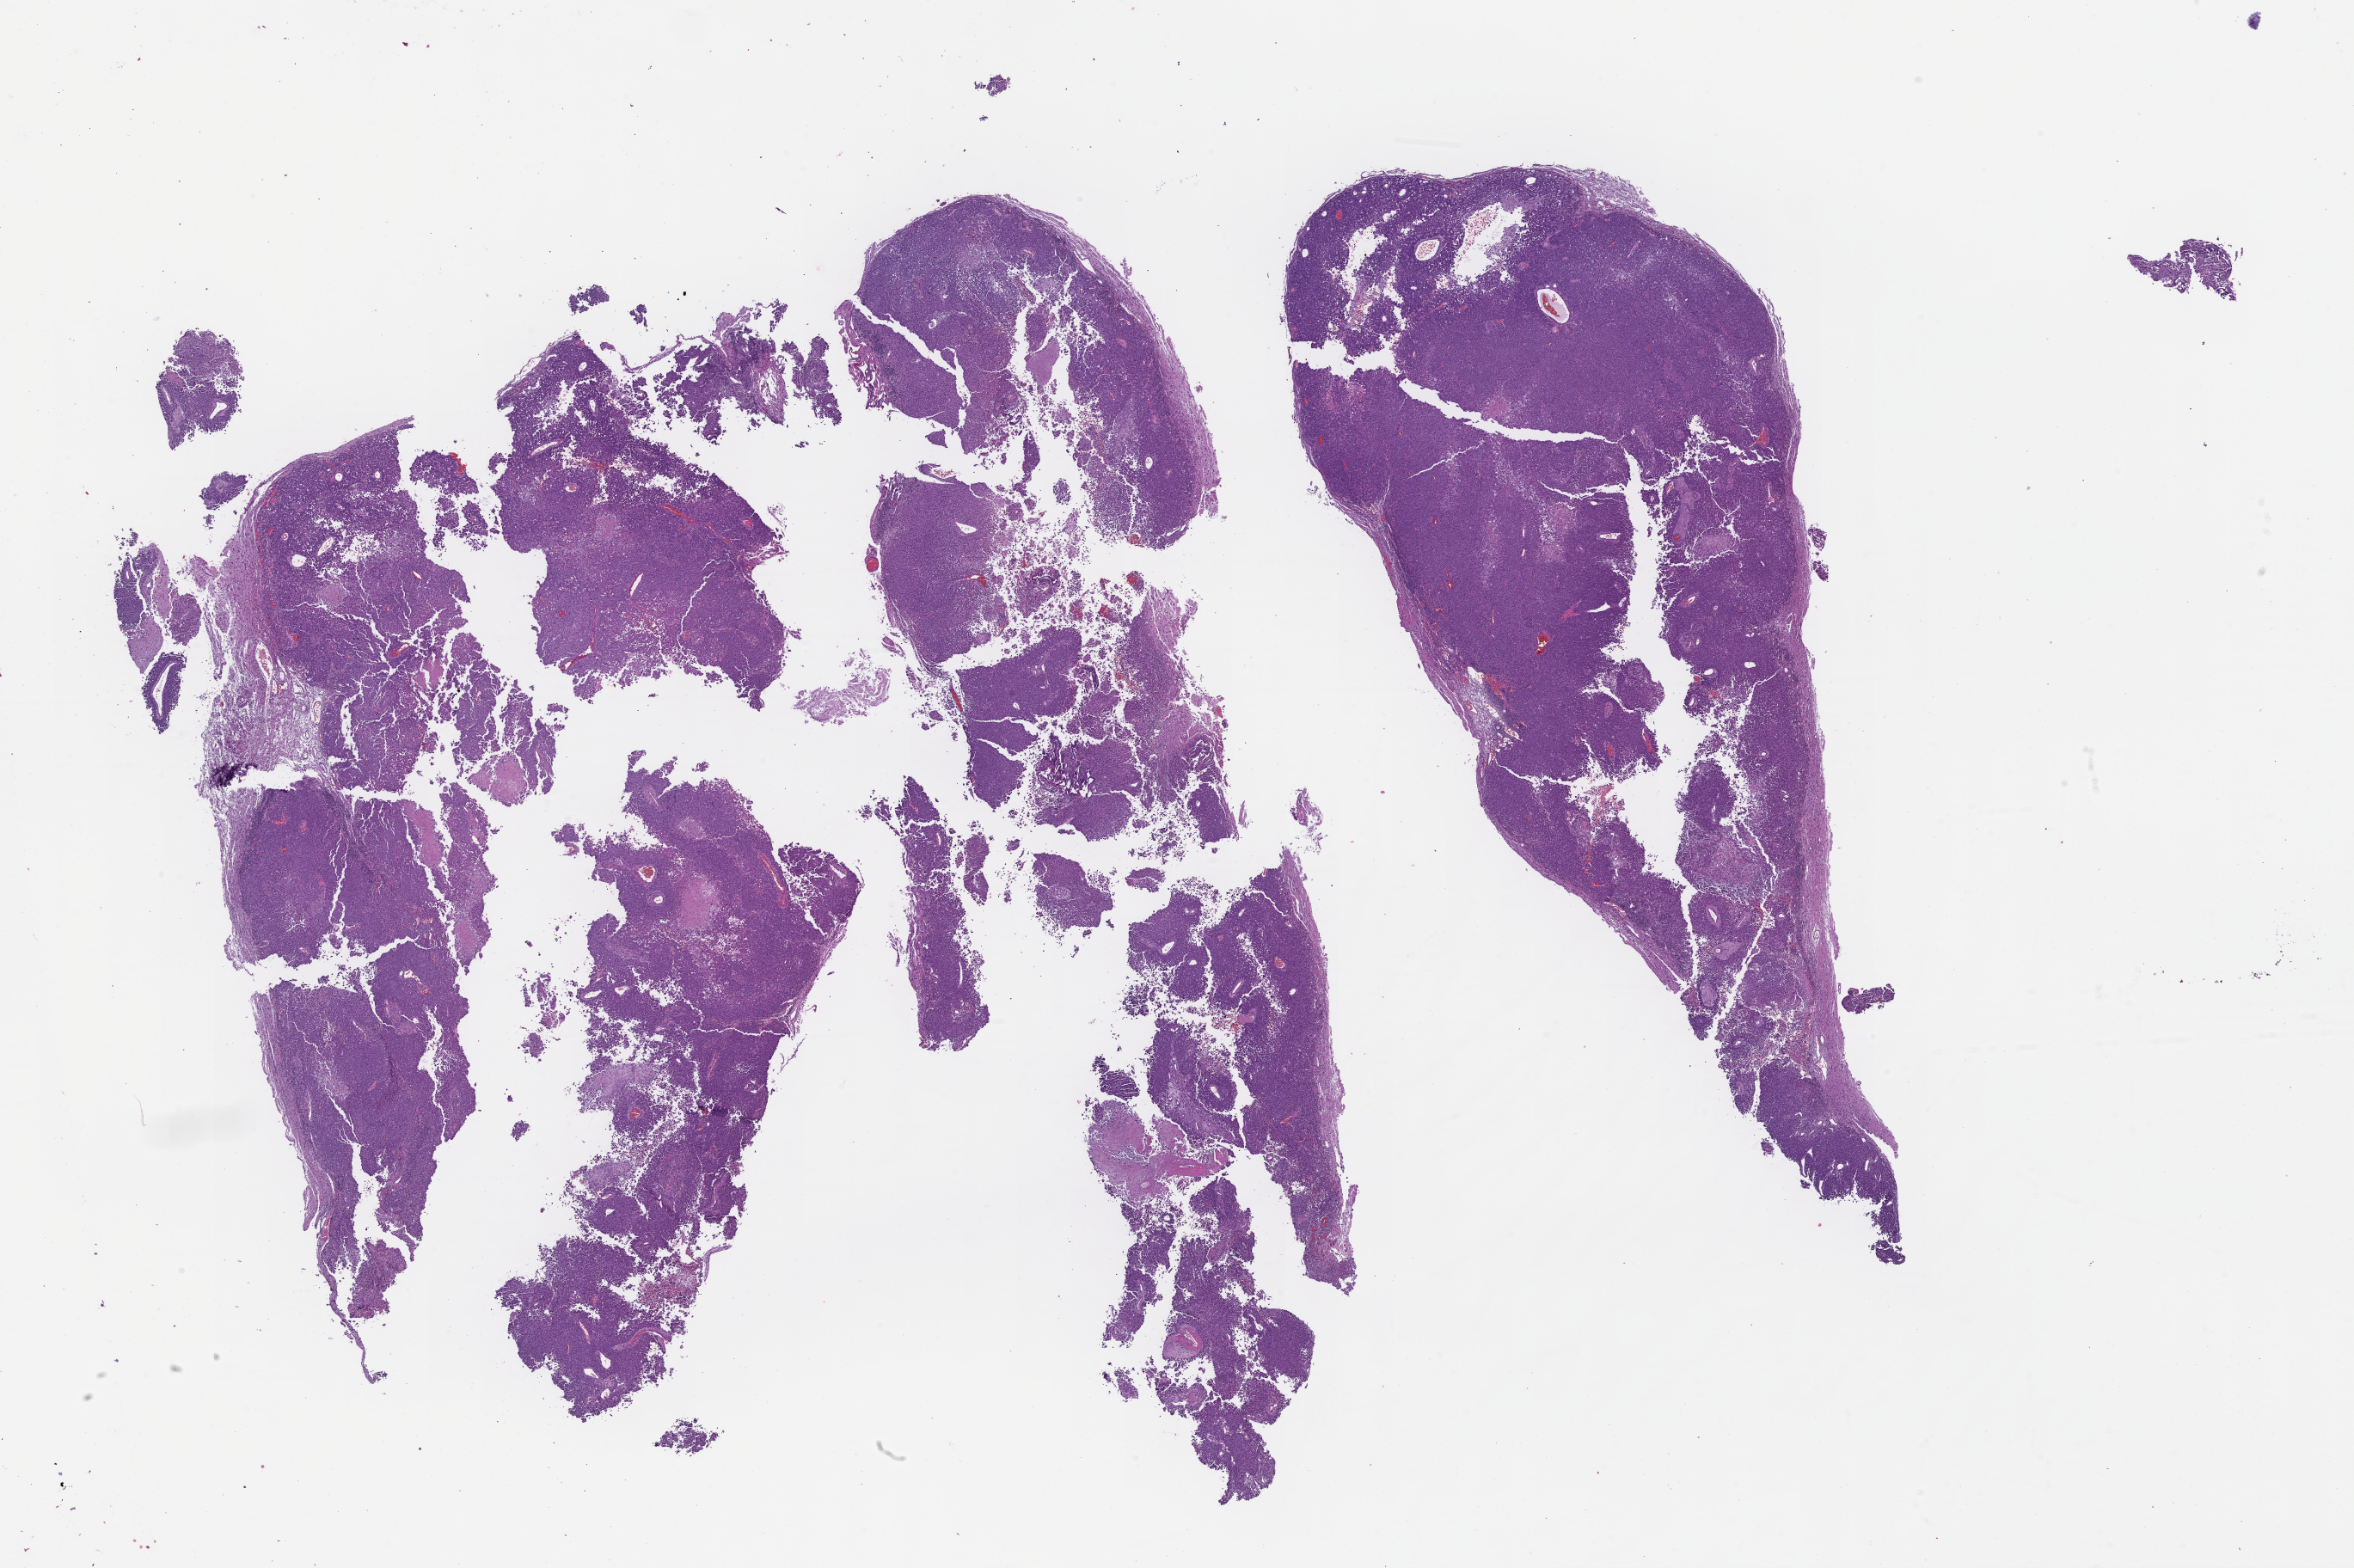
Whole-slide image, haematoxylin and eosin stain, low-resolution overview of the scanned area, about 22.1 x 14.7 mm. FFPE section. Specimen time point: archival tissue. Male patient.
This section: metastasis (sampled organ not recorded). Patient diagnosis (primary): Melanoma.